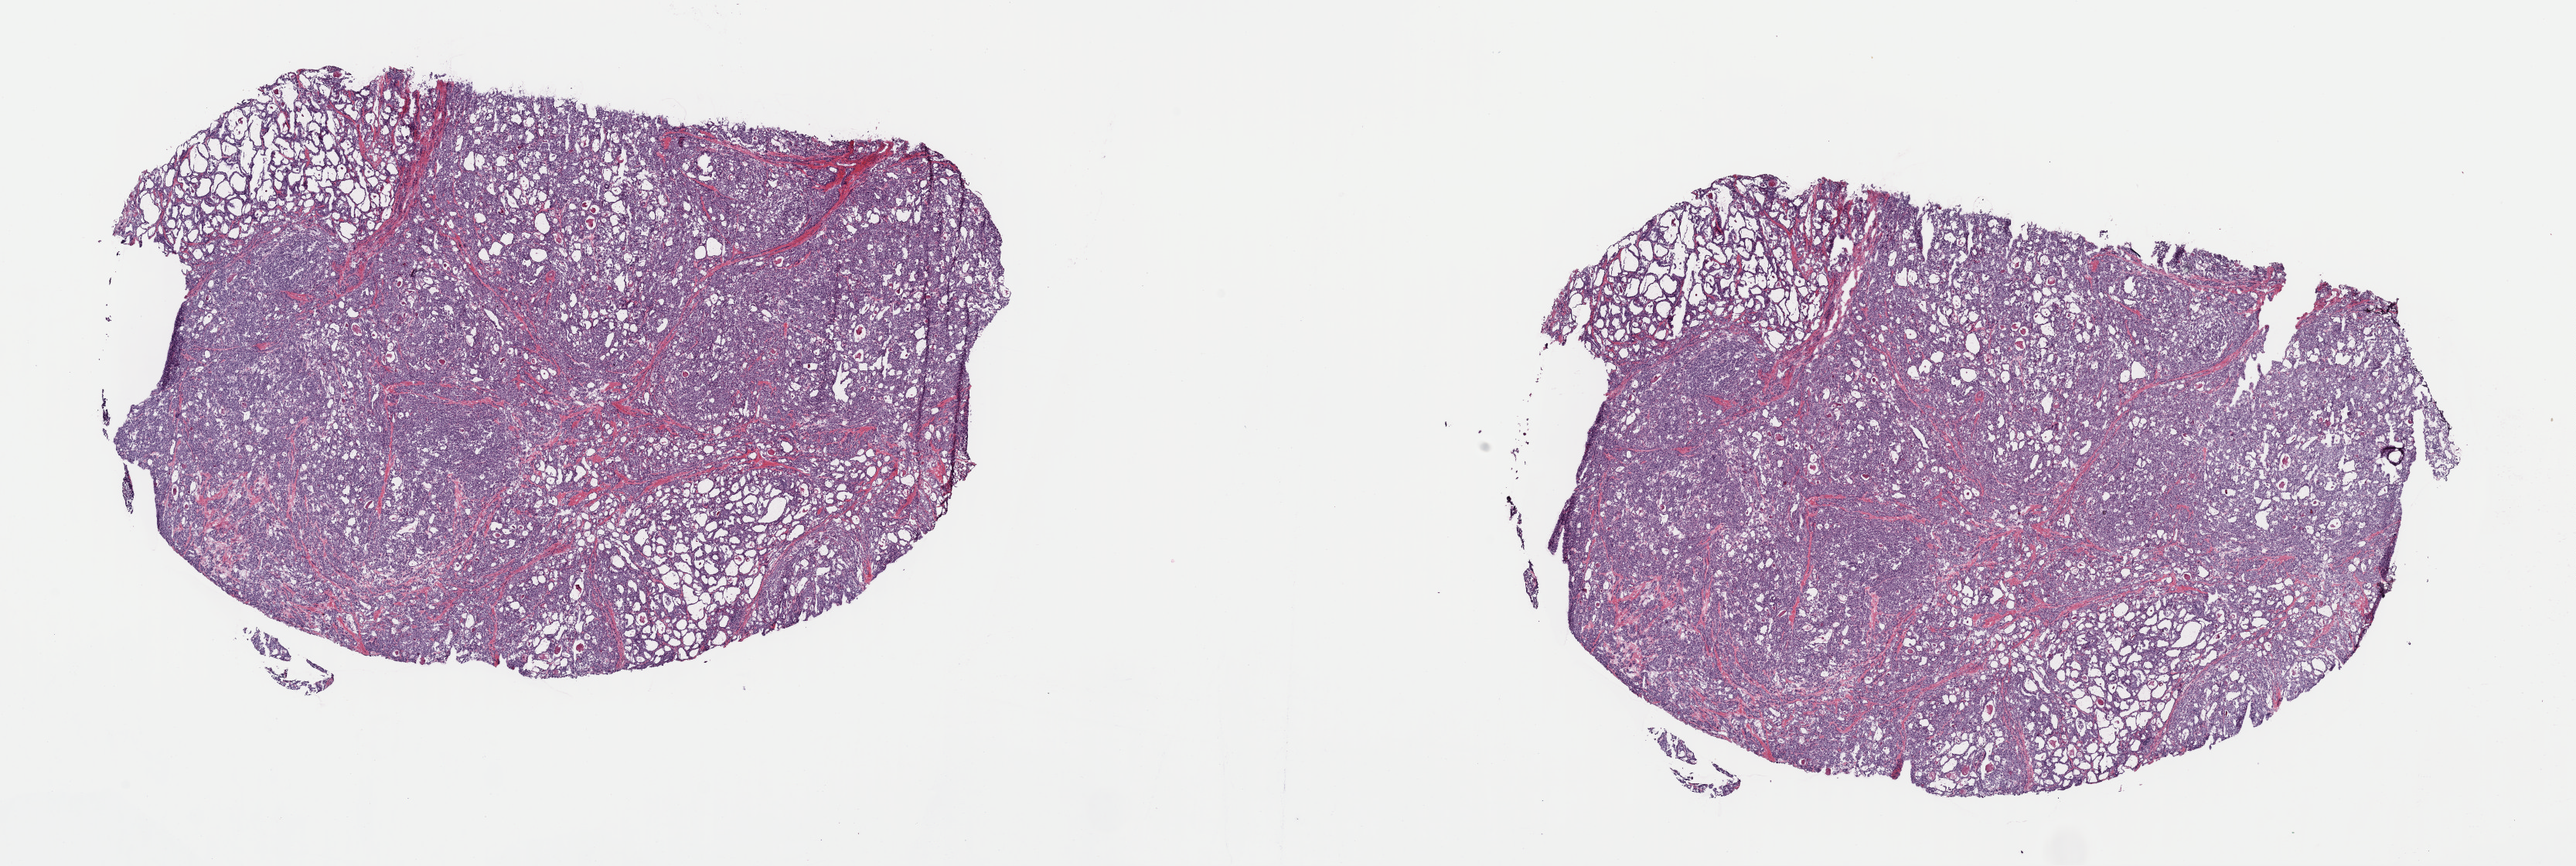
H&E-stained whole-slide image, whole scanned area (about 26.3 x 8.8 mm, acquisition: 40x scan) shown as a low-resolution overview, frozen section from the top of the tissue portion, sample: primary tumour, thyroid. Female patient; age at initial diagnosis 36 years. Slide review estimates, as recorded: tumour cells 85%, tumour nuclei 100%, normal cells 0%, stromal cells 15%, necrosis 0%. Inflammatory infiltration, as recorded: lymphocyte infiltration 0%, monocyte infiltration 1%, neutrophil infiltration 0%.
Laterality: right. Pathologic diagnosis: Papillary carcinoma, follicular variant (thyroid gland). AJCC pathologic stage: II (7th edition). TNM: T3 N1b M1.